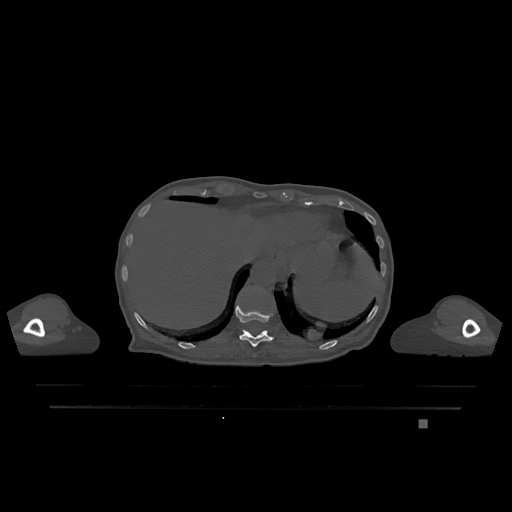
CT including the spine, one axial slice. Position 579 of 1317 along the scan axis. Bone window (W 1800 / L 400 HU). 0.5 mm slice thickness. 512 × 512 image matrix. Female patient, age 74 years. From the clinical record (not read from this slice): primary cancer: lung; vertebrae with lytic lesions (as recorded): T1, T4, T5, T6, L4, L5.
Structures marked on this image (semi-automatically segmented with operator editing):
- T11 vertebra: bounding box (x1, y1, x2, y2) in pixels: (235, 300, 274, 347)